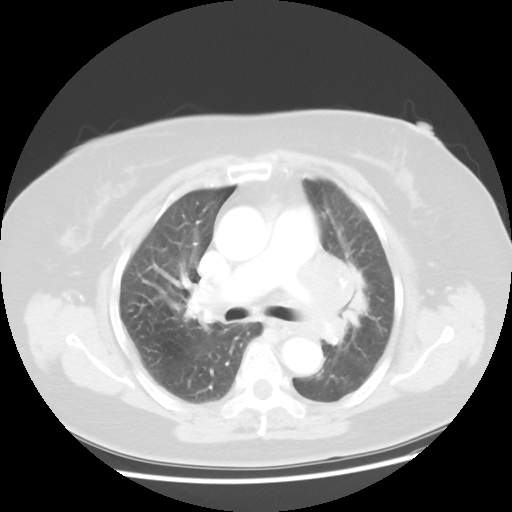
Chest CT, one axial slice; slice 28 of 49 in the series (ordered by position); lung window (W 1500 / L -600 HU); 5 mm slice thickness; 512 × 512 image matrix. Female patient, age 58 years. From the clinical record (not read from this slice): clinical TNM (as recorded): T4 N3 M0; histopathological grade: G3.
Outlined on this slice (rectangle marked by the reading radiologist):
- lung tumour (recorded histology: small cell carcinoma): box from (x=285, y=243) to (x=368, y=386) px